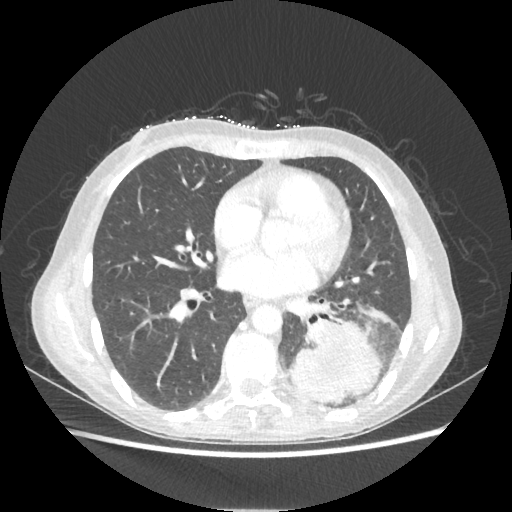
Chest CT, one axial slice; position 98 of 221 along the scan axis; 80 kVp; lung window (W 1500 / L -600 HU); 1.25 mm slice thickness; 512 × 512 image matrix. Patient: female, 53 years. From the clinical record (not read from this slice): clinical TNM (as recorded): T3 N0 M0.
Structures marked on this image (bounding box drawn by a radiologist):
- lung tumour (recorded histology: adenocarcinoma): bounding box <286,319,380,404> (left, top, right, bottom; pixels)